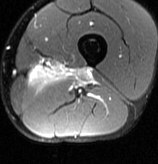
MRI of an extremity soft-tissue mass, one axial slice. Position 20 of 70 along the scan axis. T2-weighted fat-saturated. MR volume resampled by the dataset authors to the PET/CT grid (not the native acquisition matrix). 158 × 164 image matrix, field of view 154 × 160 mm. Male patient. From the clinical record (not read from this slice): histological type: extraskeletal osteosarcoma; grade: high; site of the primary tumour: left adductur.
Structures marked on this image (expert contour drawn on MRI and transferred to this co-registered scan by the dataset authors):
- gross tumour volume (mass): box from (x=26, y=64) to (x=94, y=93) px